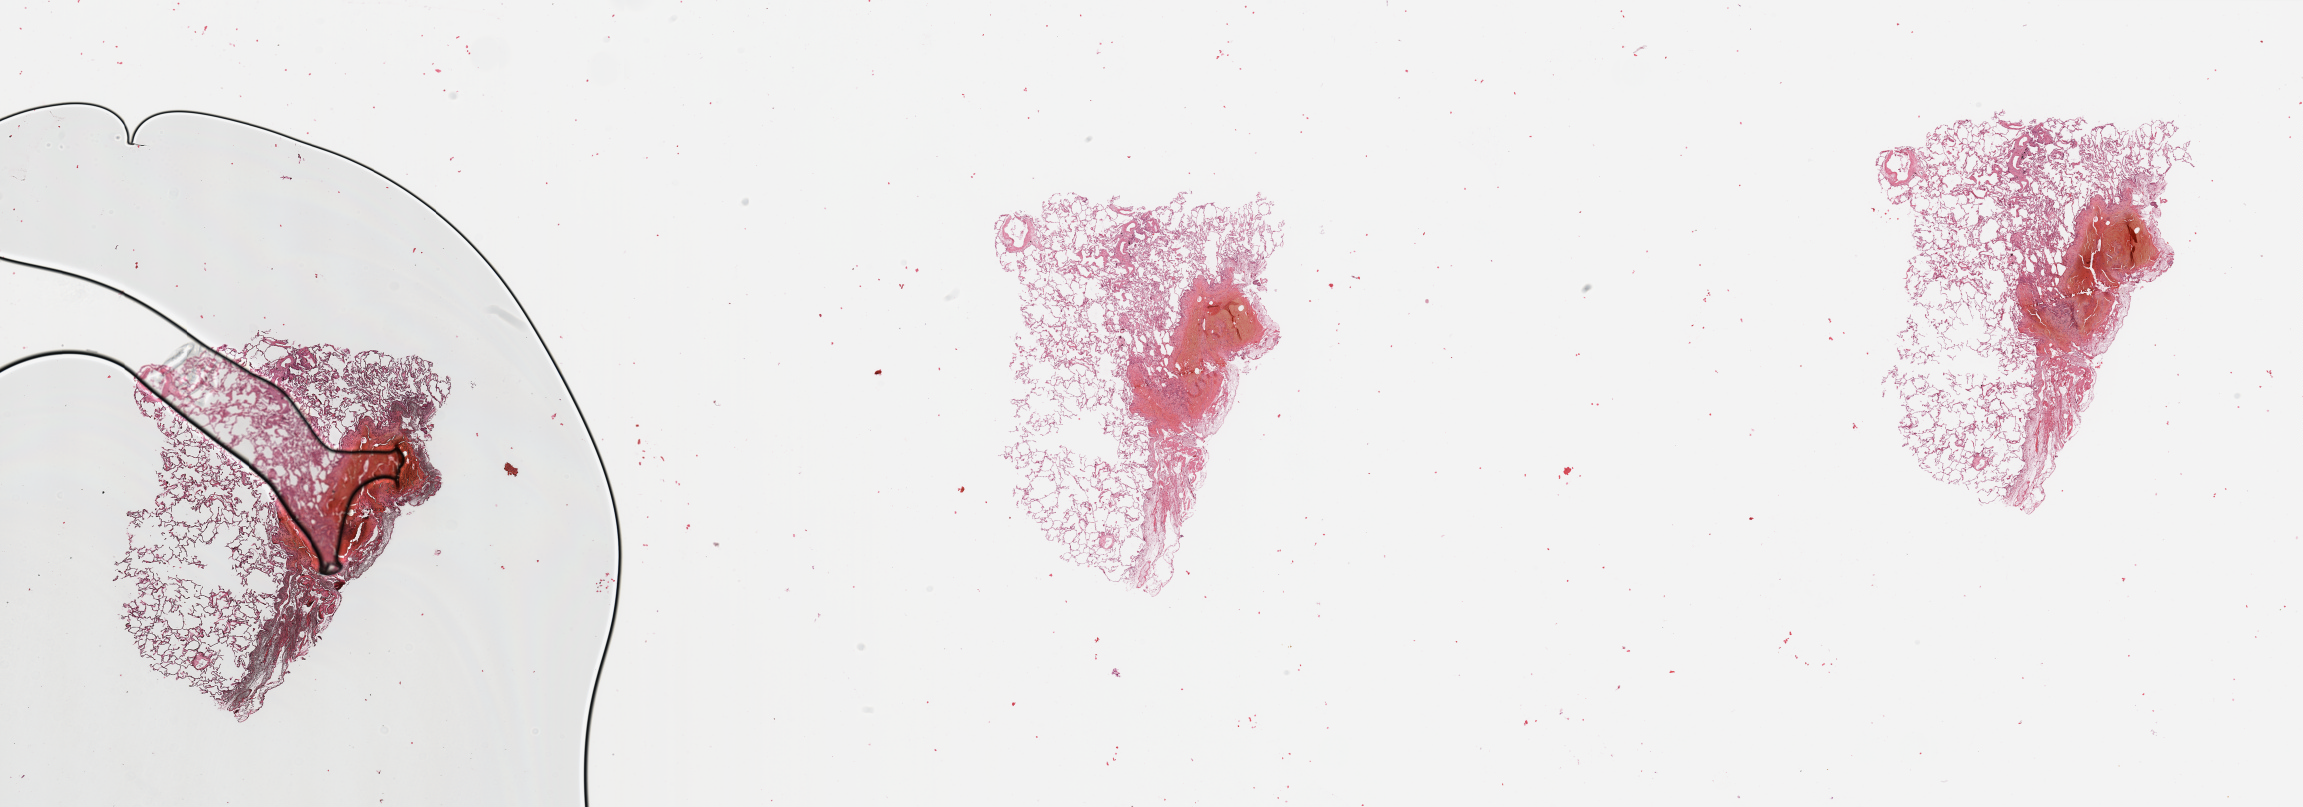
Digitized Hematoxylin and eosin (H&E) stained tissue section (whole slide) — low-resolution overview of the scanned area, about 36.4 x 12.8 mm (from a 20x scan); normal (non-tumour) tissue sample, sampled site: lung. Patient: female, age 66 years.
• this section: normal (non-tumour) tissue from the same patient
• patient diagnosis: Adenocarcinoma, NOS